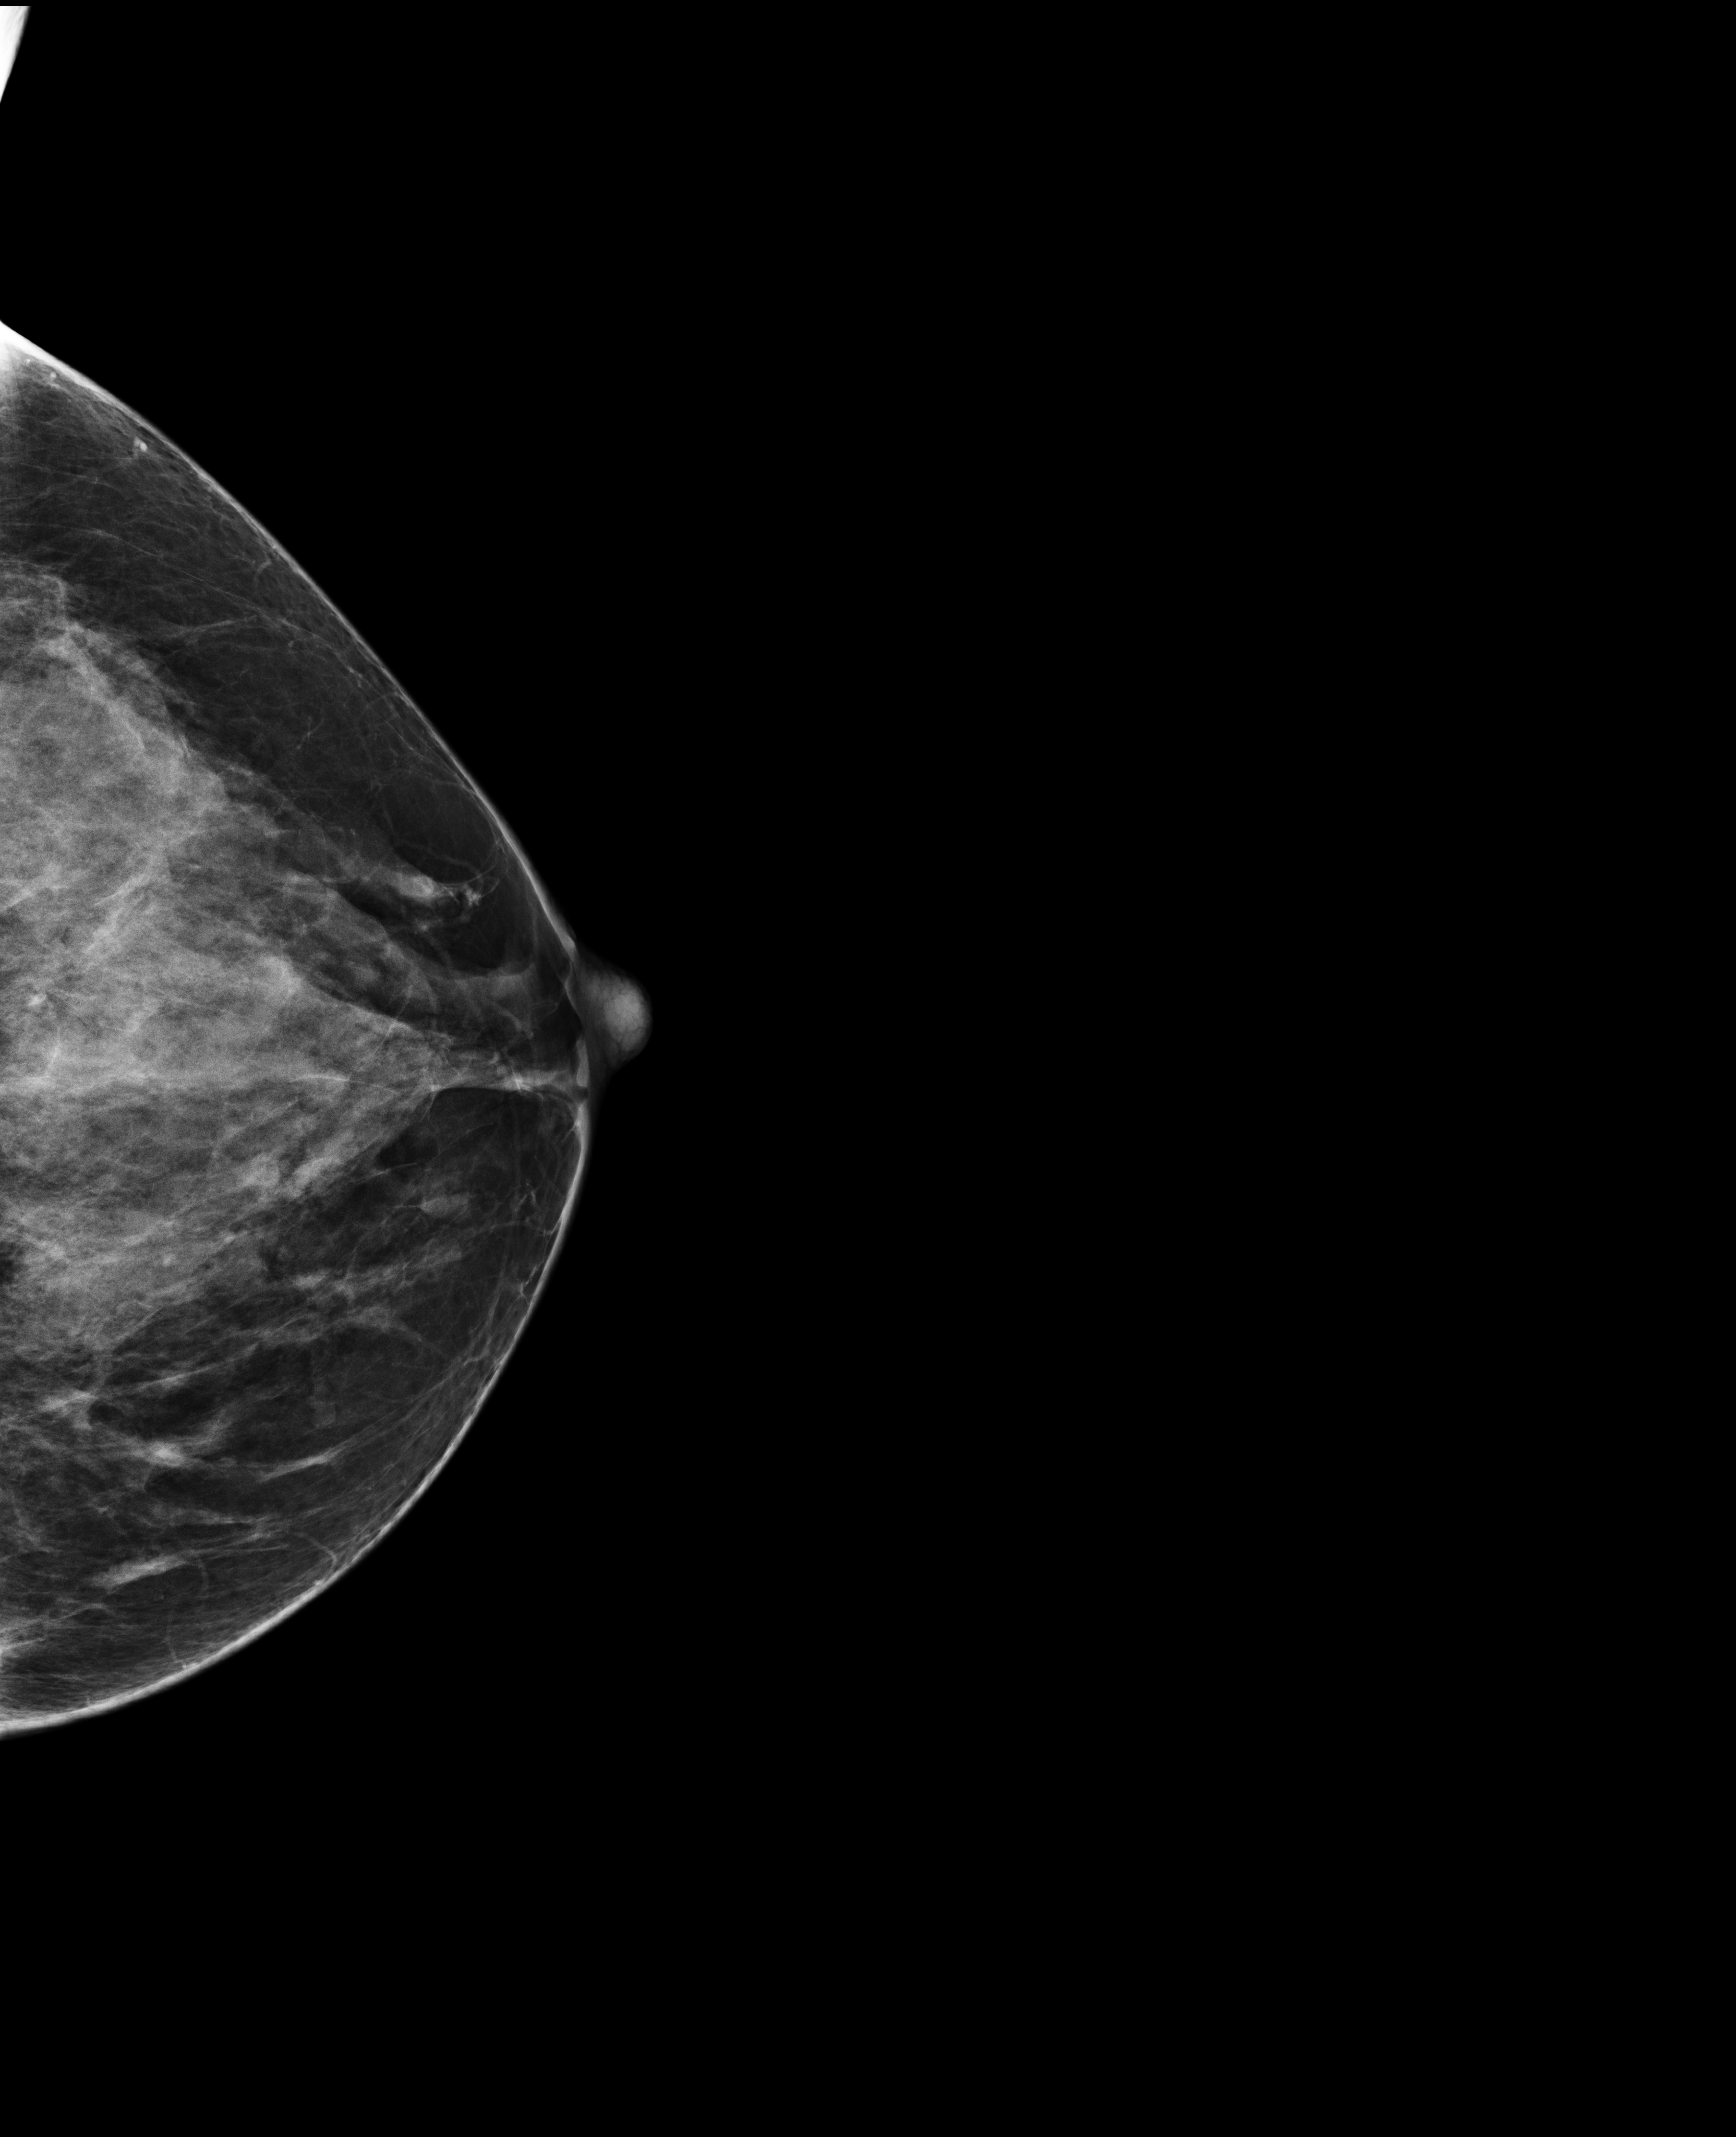
Digital mammogram (FFDM), left breast, craniocaudal (CC) view, annual screening mammography examination, compressed breast thickness 55 mm, system: Selenia Dimensions. Patient: female, 50 years.
- BI-RADS breast density category at the screening exam (both breasts, scale 1–4): 4
- final BI-RADS assessment for this screening round (tomosynthesis exam, both breasts): category 1
- recall: no recall after this screen